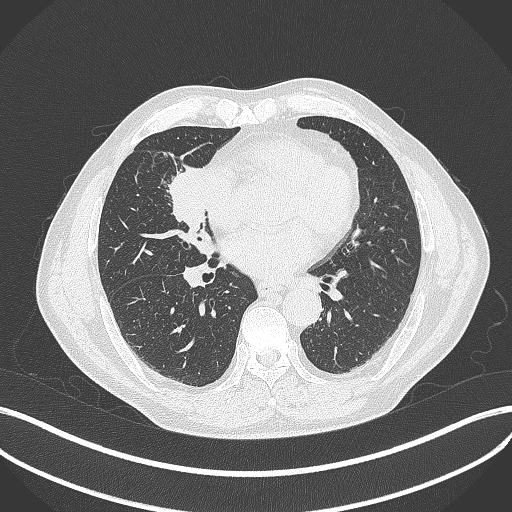
Chest CT, one axial slice; position 183 of 429 along the scan axis; lung window (W 1500 / L -600 HU); 1 mm slice thickness; 512 × 512 image matrix. Male patient, age 61 years. Case-level facts recorded for this patient, not image findings: clinical TNM (as recorded): T2b N1 M0.
Annotated regions visible in this slice (bounding box drawn by a radiologist):
- lung tumour (recorded histology: squamous cell carcinoma): bounding box (x1, y1, x2, y2) in pixels: (162, 159, 214, 242)